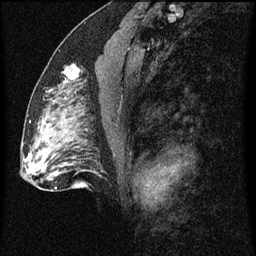
Breast MRI (dynamic contrast-enhanced), one sagittal slice. Slice 36 of 60 in the series (ordered by position). Dynamic contrast-enhanced series, image 2 of 3 at this slice position (ordered by acquisition). 1.5 T. TE 4.2 ms, TR 8 ms. 2 mm slice thickness. 256 × 256 image matrix. Patient: female, 51 years.
Annotated regions visible in this slice (semi-automatic segmentation, software-assisted and operator-edited):
- analysis volume of interest (the breast-tissue region the enhancement analysis was run in; not a lesion): box from (x=54, y=50) to (x=95, y=103) px
- tumour enhancement mask (voxels above the 70 % enhancement threshold inside the analysis volume of interest): (x=64, y=66)–(x=81, y=75)